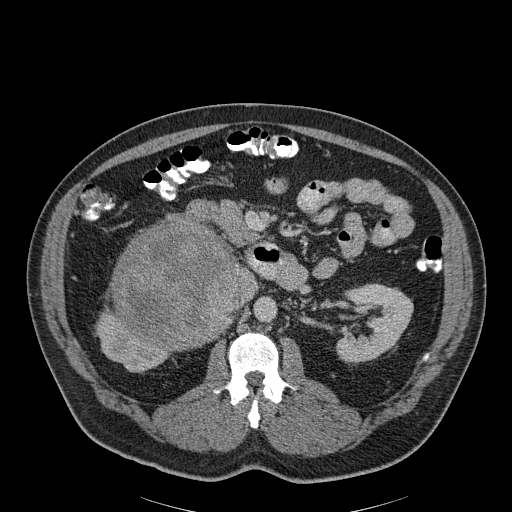
Contrast-enhanced abdominal CT, one axial slice; slice 113 of 186 in the series (ordered by position); reconstruction kernel B30f; 120 kVp; soft-tissue window (W 400 / L 40 HU); 3 mm slice thickness; 512 × 512 image matrix, field of view 464 × 464 mm. Patient: male, 56 years. From the clinical record (not read from this slice): diagnosis: adrenocortical carcinoma; tumour side: right adrenal; tumour size at pathology: 18 cm; Ki-67 index: 2 %; stage (as recorded): 3.
Outlined on this slice (semi-automatic segmentation, software-assisted and operator-edited):
- mass: box from (x=113, y=221) to (x=235, y=349) px